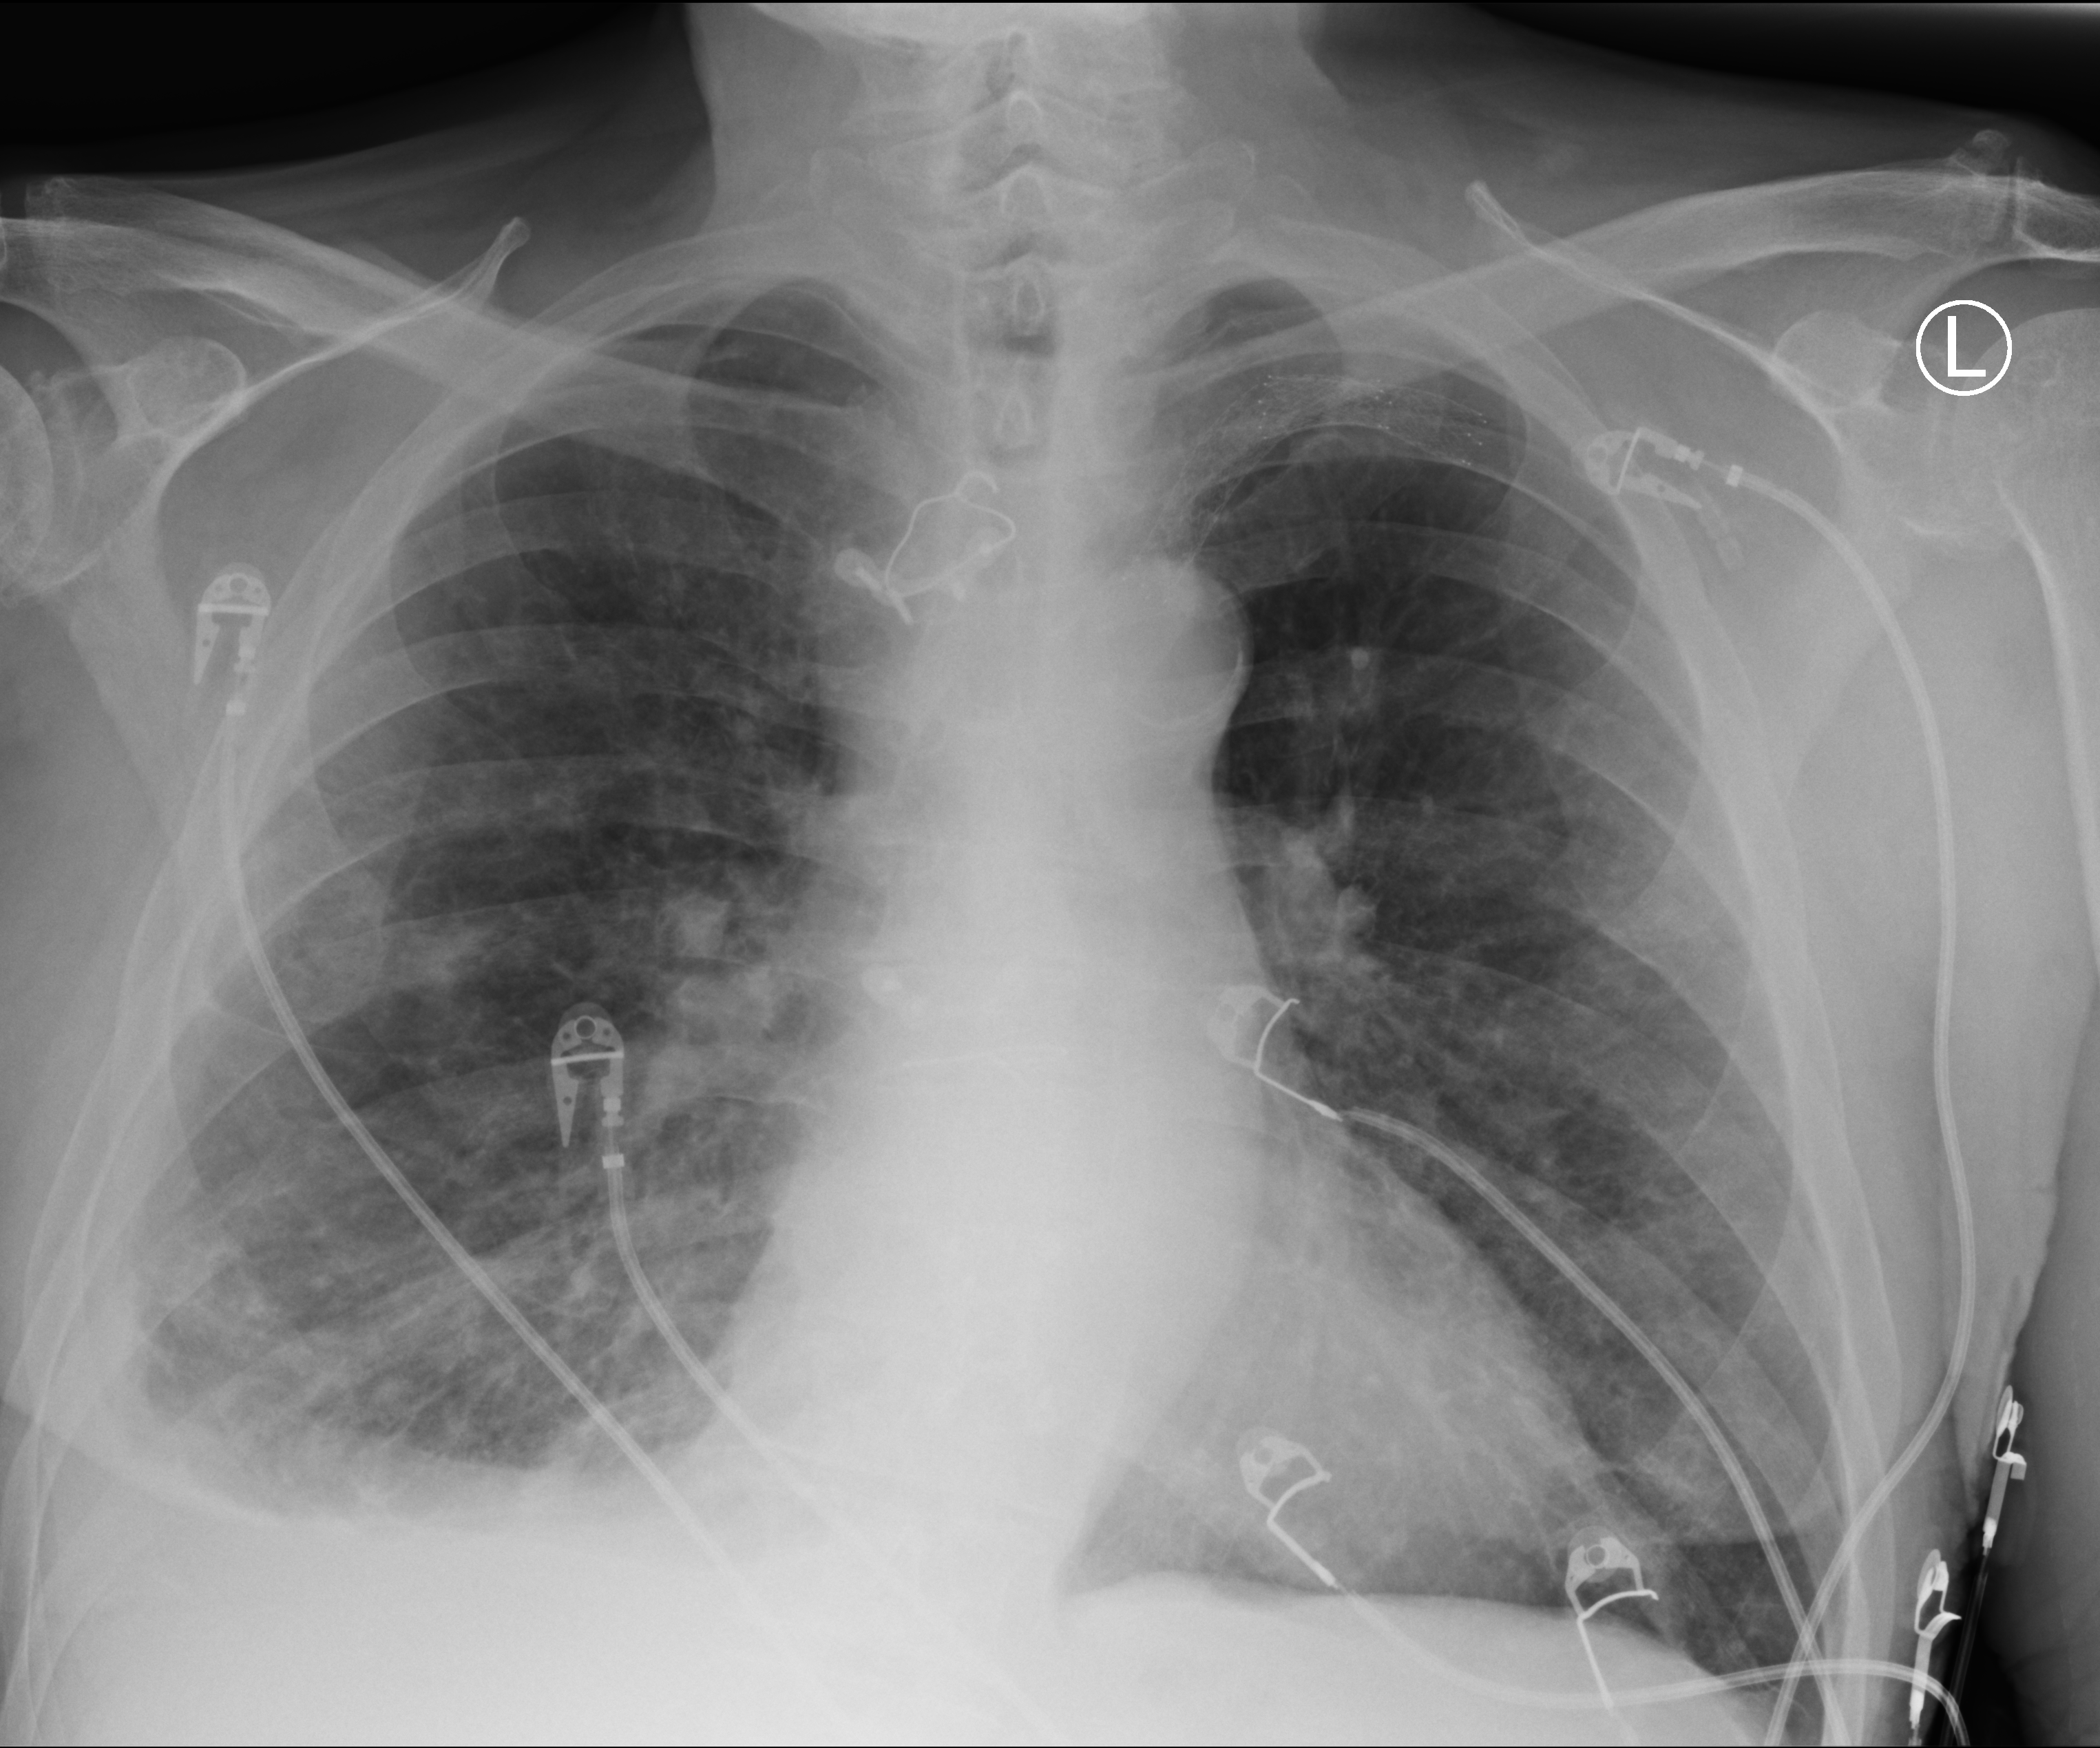
Portable chest radiograph; anteroposterior (AP) projection. Male patient hospitalised with COVID-19, age 75–90 years.
Admission-level facts for this patient (not findings on this image; timing relative to this image not recorded): admitted to intensive care during this hospital stay: no; mechanically ventilated during this hospital stay: no.